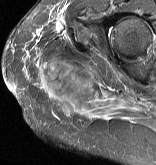
MRI of an extremity soft-tissue mass, one axial slice; STIR; MR volume resampled by the dataset authors to the PET/CT grid (not the native acquisition matrix); 3.27 mm slice thickness; 156 × 165 image matrix, field of view 152 × 161 mm. Female patient. Case-level facts recorded for this patient, not image findings: histological type: epithelioid sarcoma with vascular differentiation; site of the primary tumour: right buttock.
Annotated regions visible in this slice (expert contour drawn on MRI and transferred to this co-registered scan by the dataset authors):
- gross tumour volume (mass): box from (x=38, y=58) to (x=94, y=109) px